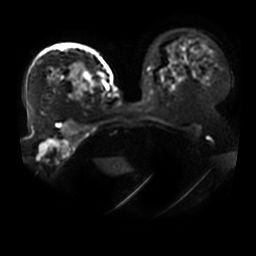
Breast MRI, one axial slice. Position 30 of 41 along the scan axis. Diffusion-weighted series; image 2 of 4 stored at this slice position (different b-values; order by instance number). 3 T. 5 mm slice thickness. 256 × 256 image matrix, field of view 400 × 400 mm. Female patient.
Annotated regions visible in this slice (expert manual segmentation):
- tumour on diffusion-weighted imaging: box from (x=69, y=67) to (x=87, y=99) px